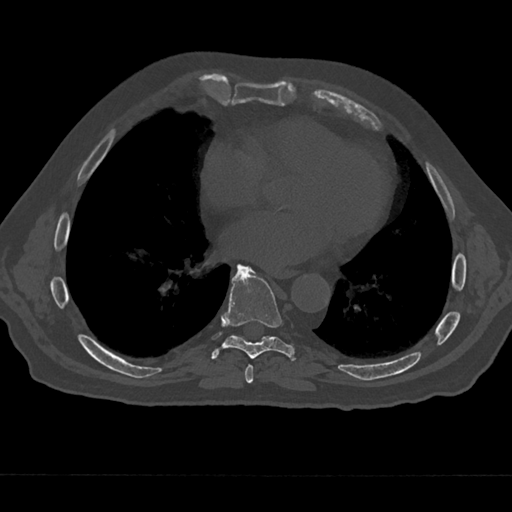
CT including the spine, one axial slice. Position 313 of 797 along the scan axis. Reconstruction kernel Br40s/3. Bone window (W 1800 / L 400 HU). 0.5 mm slice thickness. 512 × 512 image matrix, field of view 377 × 377 mm. Patient: male, 75 years. From the clinical record (not read from this slice): primary cancer: renal; vertebrae with lytic lesions (as recorded): T4.
Structures marked on this image (semi-automatically segmented with operator editing):
- T7 vertebra: box from (x=240, y=364) to (x=255, y=384) px
- T8 vertebra: (x=211, y=265)–(x=296, y=362)